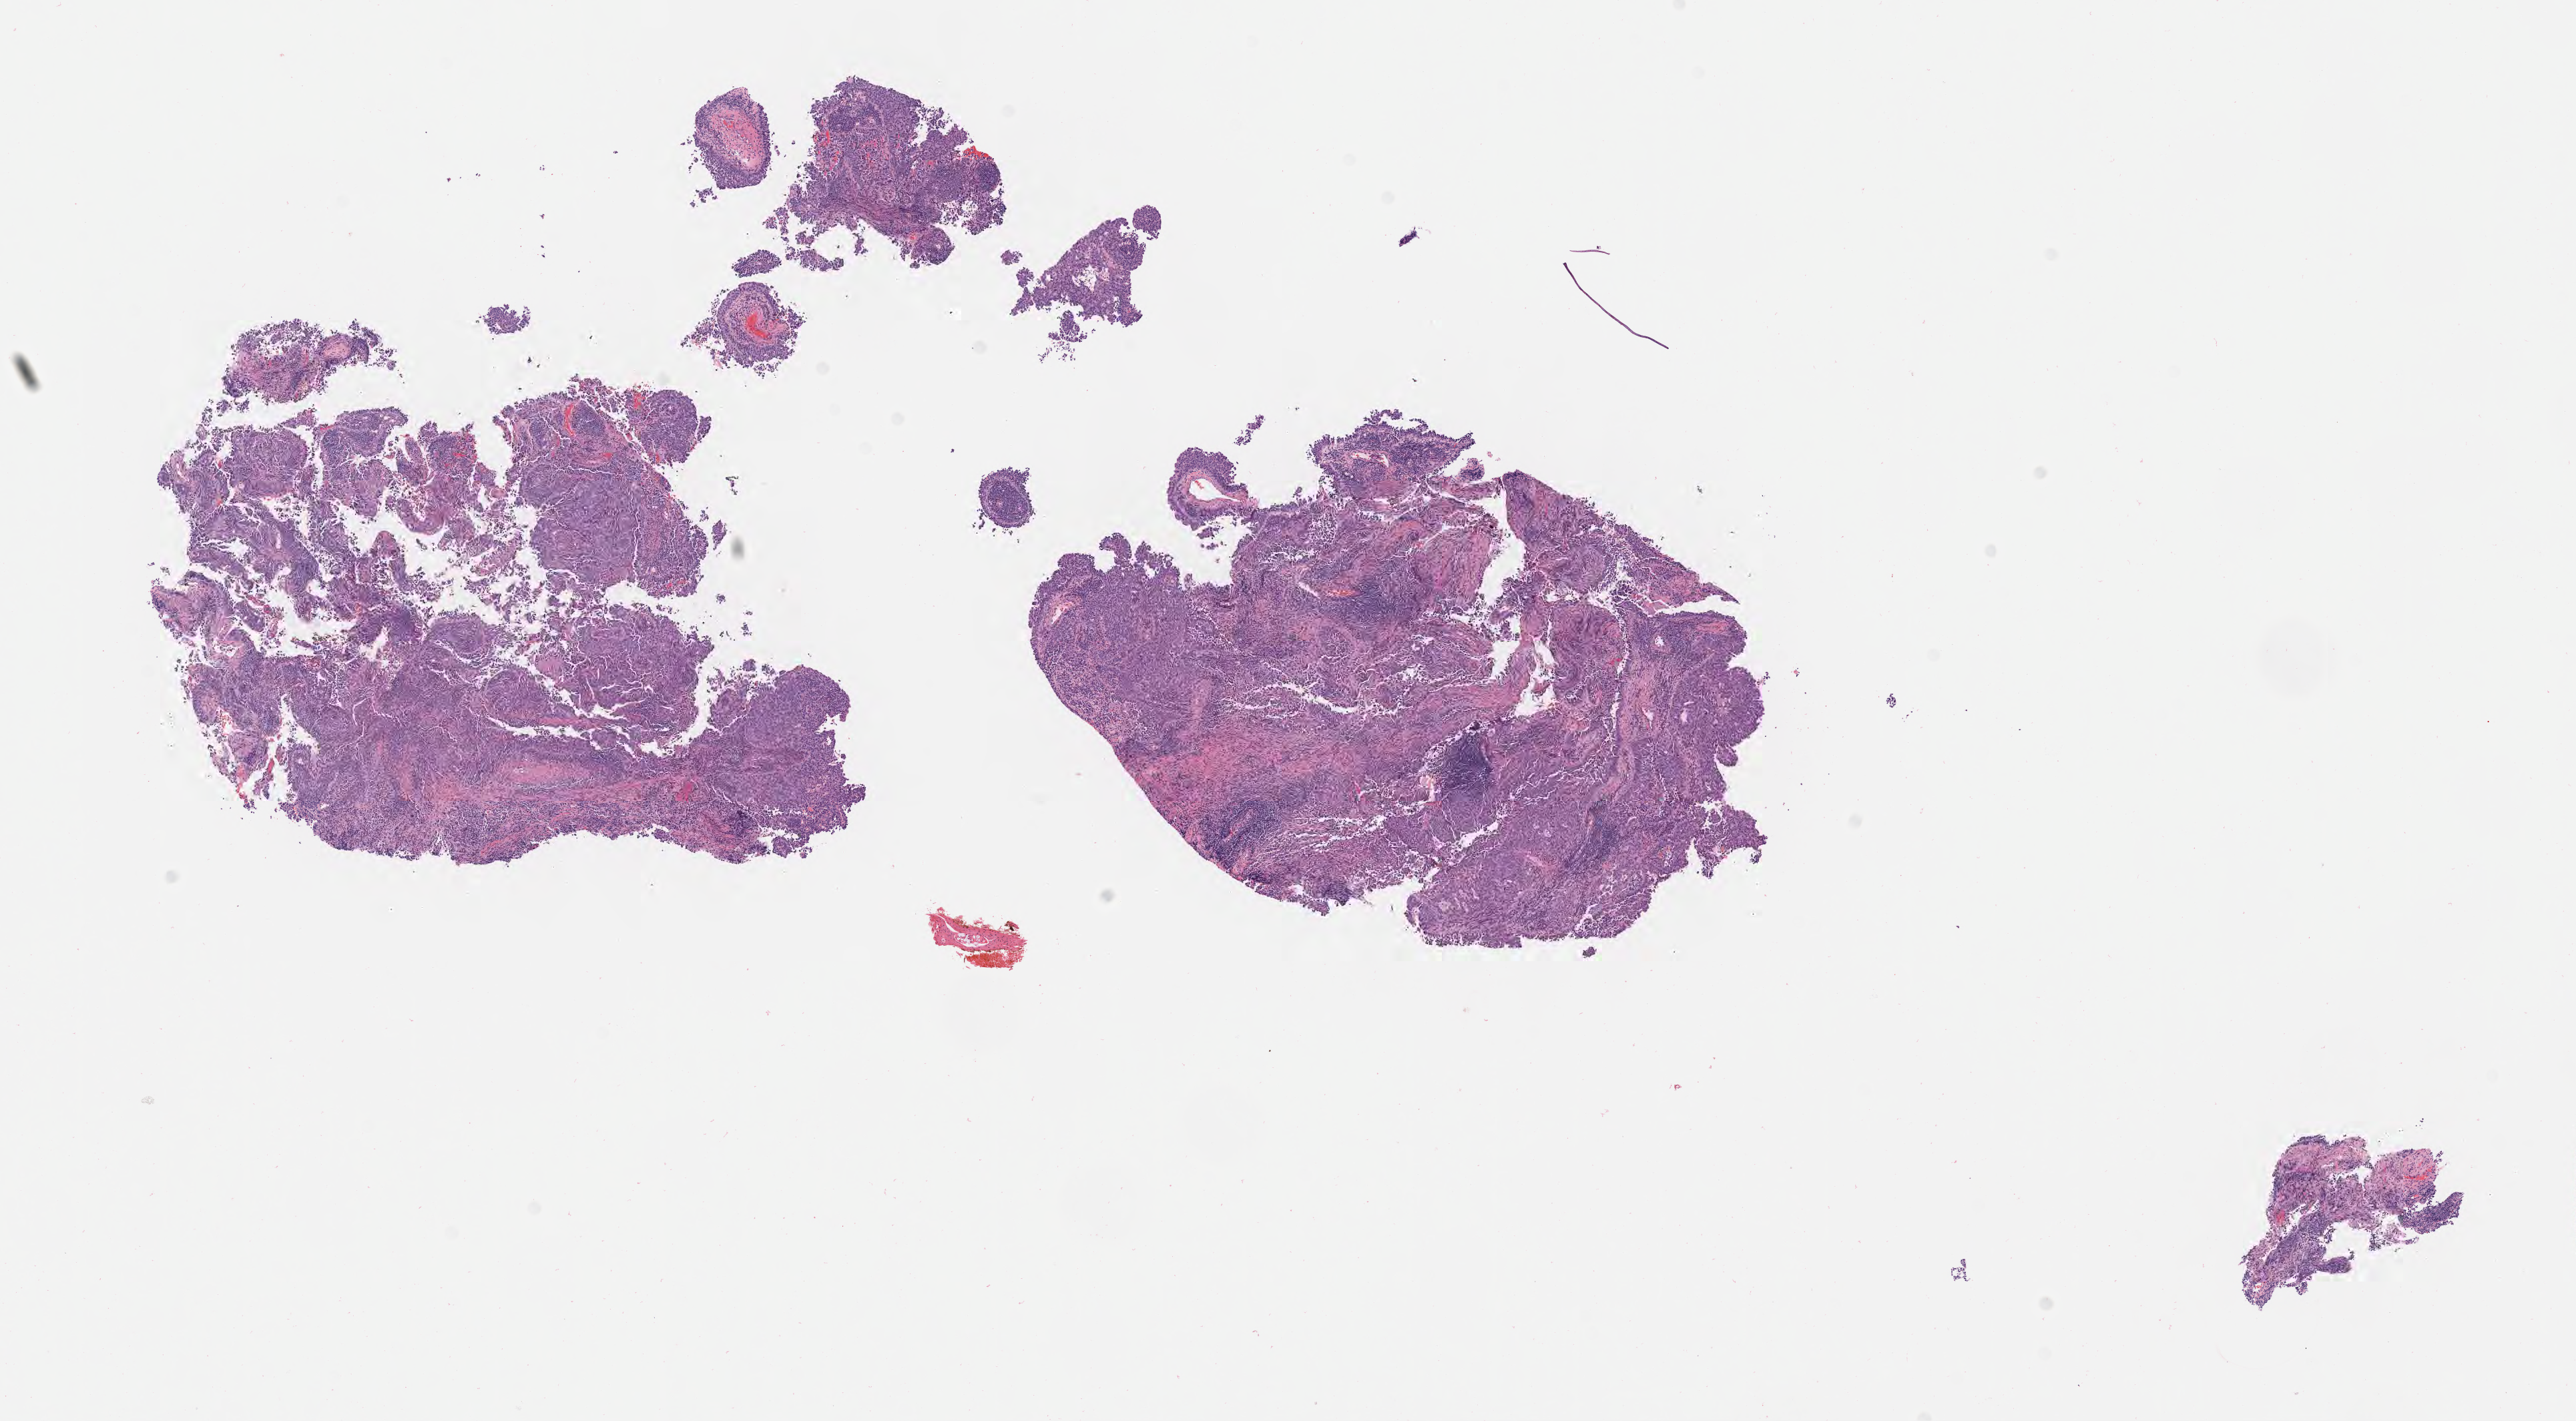
Hematoxylin and eosin (H&E) whole-slide image — whole scanned area (about 15.6 x 8.6 mm) shown as a low-resolution overview. Tumor tissue. Anatomic site: cervix. Patient female; aged 65.
Diagnosis: Squamous cell carcinoma, large cell, nonkeratinizing, NOS.